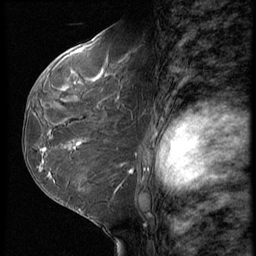
Breast MRI (dynamic contrast-enhanced), one sagittal slice. 3 images stored at this slice position (order not interpretable as contrast timing). 1.5 T. TE 4.2 ms, TR 9 ms. 2.5 mm slice thickness. 256 × 256 image matrix, field of view 180 × 180 mm. Female patient, age 50 years. Case-level facts recorded for this patient, not image findings: setting: breast cancer imaged before/during neoadjuvant chemotherapy; receptor status: HR-positive, HER2-negative.
Annotated regions visible in this slice (semi-automatically segmented with operator editing):
- analysis volume of interest (the breast-tissue region the enhancement analysis was run in; not a lesion): box from (x=32, y=91) to (x=118, y=209) px
- tumour enhancement mask (voxels above the 140 % enhancement threshold inside the analysis volume of interest): (x=45, y=140)–(x=87, y=150)